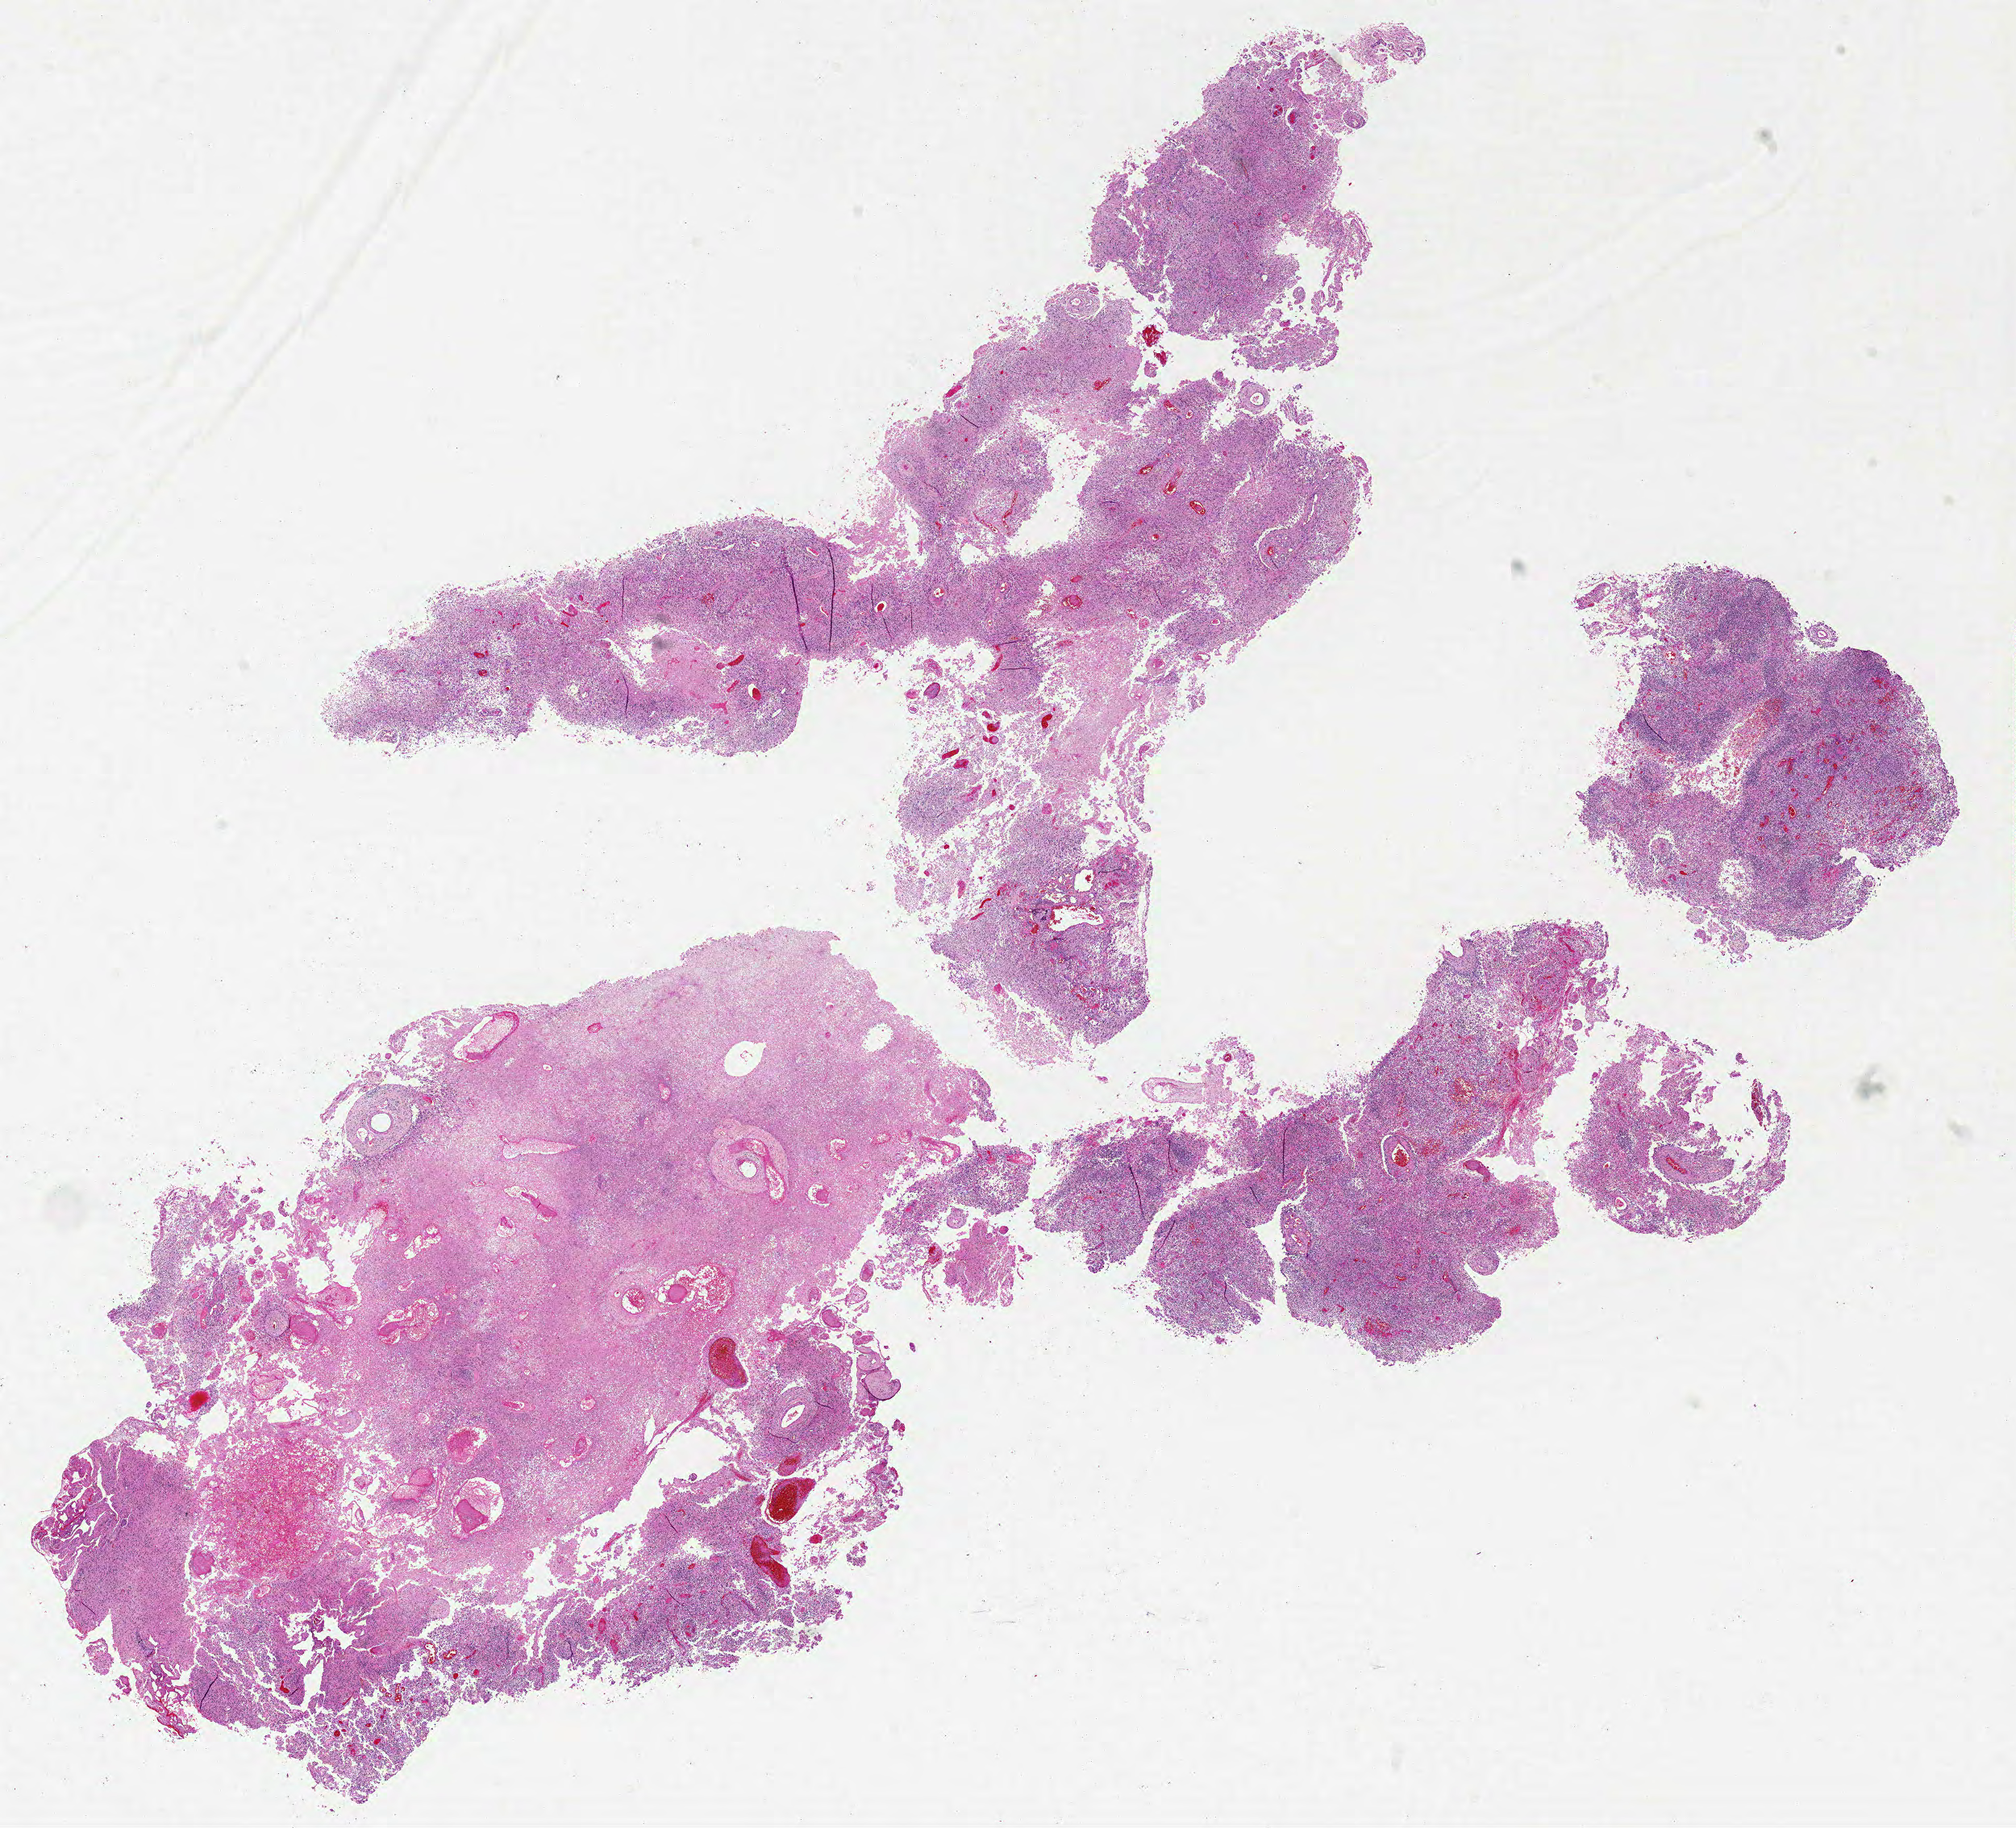
Whole-slide histology image, H&E-stained, shown as a low-resolution overview of the whole scanned area (about 20.0 x 18.1 mm). Formalin-fixed paraffin-embedded (FFPE) diagnostic section. Primary tumour sample from the brain. Patient: male, age at initial diagnosis 57 years.
* diagnosis: Glioblastoma